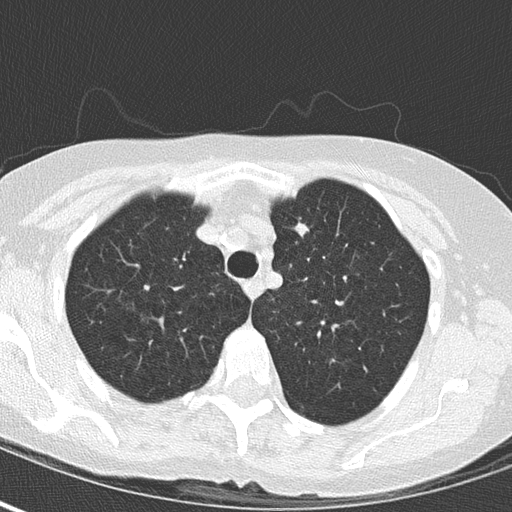
Low-dose screening chest CT, axial slice. Second screening round (one year after baseline). Lung window (W 1500 / L -600 HU). Lung (sharp) reconstruction kernel (B50f). Slice 39 of 163 in the series. 512 × 512 image matrix, field of view 280 × 280 mm. Female, age 64 years at enrolment.
Expert-annotated lung lesion, bounding box [x1, y1, x2, y2] px = [277, 211, 324, 256]. Screening reader's record for this exam (one nodule recorded; not confirmed to be the boxed lesion): non-calcified nodule or mass ≥4 mm, left upper lobe, 8 × 7 mm, pre-existing on the prior screen: yes. Lung cancer was diagnosed 123 days after this screen: adenocarcinoma, NOS, left upper lobe, moderately differentiated (G2), stage IA (AJCC 6th edition), 7 mm at pathology.